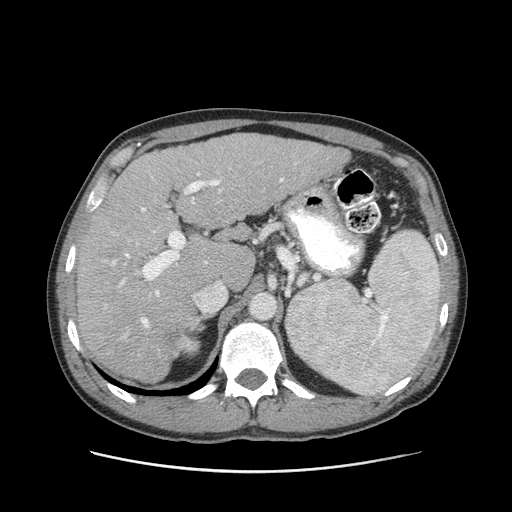
Contrast-enhanced abdominal CT (liver protocol), one axial slice. Position 61 of 93 along the scan axis. 120 kVp. Soft-tissue window (W 400 / L 40 HU). 2.5 mm slice thickness. 512 × 512 image matrix, field of view 380 × 380 mm. Case-level facts recorded for this patient, not image findings: diagnosis: hepatocellular carcinoma (patient treated with transarterial chemoembolisation; whether this scan precedes or follows treatment is not stated here); TNM stage (as recorded): Stage-II; Child-Pugh class: A; tumour differentiation: moderately differentiated; tumour nodularity: multinodular.
Structures marked on this image (semi-automatic segmentation, software-assisted and operator-edited):
- liver parenchyma outside the tumour (the mass and vessels are separate outlines, so this box may not span the whole liver): bounding box <78,134,348,382> (left, top, right, bottom; pixels)
- liver vessels: <112,163,297,328>